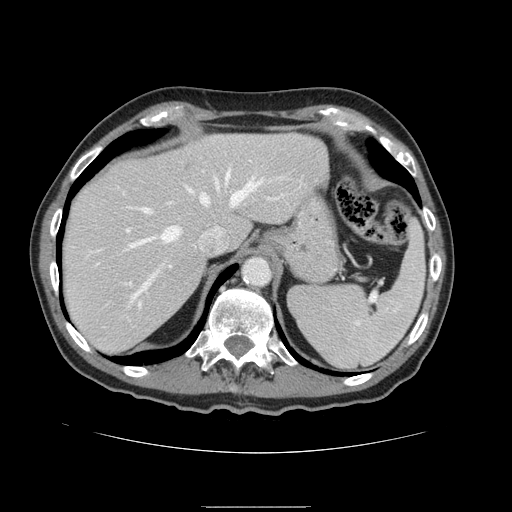
Contrast-enhanced abdominal CT, one axial slice; slice 118 of 168 in the series (ordered by position); intravenous contrast given; soft-tissue window (W 400 / L 40 HU); 512 × 512 image matrix, field of view 386 × 386 mm. Male patient, age 74 years. Case-level facts recorded for this patient, not image findings: diagnosis: colorectal cancer liver metastases, imaged before liver resection; multiple liver metastases: no; largest metastasis: 14.5 cm; disease in both lobes: yes.
Structures marked on this image (outlined manually by an expert reader):
- hepatic veins: bounding box (x1, y1, x2, y2) in pixels: (128, 170, 287, 303)
- liver: (62, 133, 328, 354)
- planned liver remnant (the part of the liver to remain after resection): (62, 133, 327, 354)
- portal vein (with intrahepatic branches): (128, 198, 278, 232)